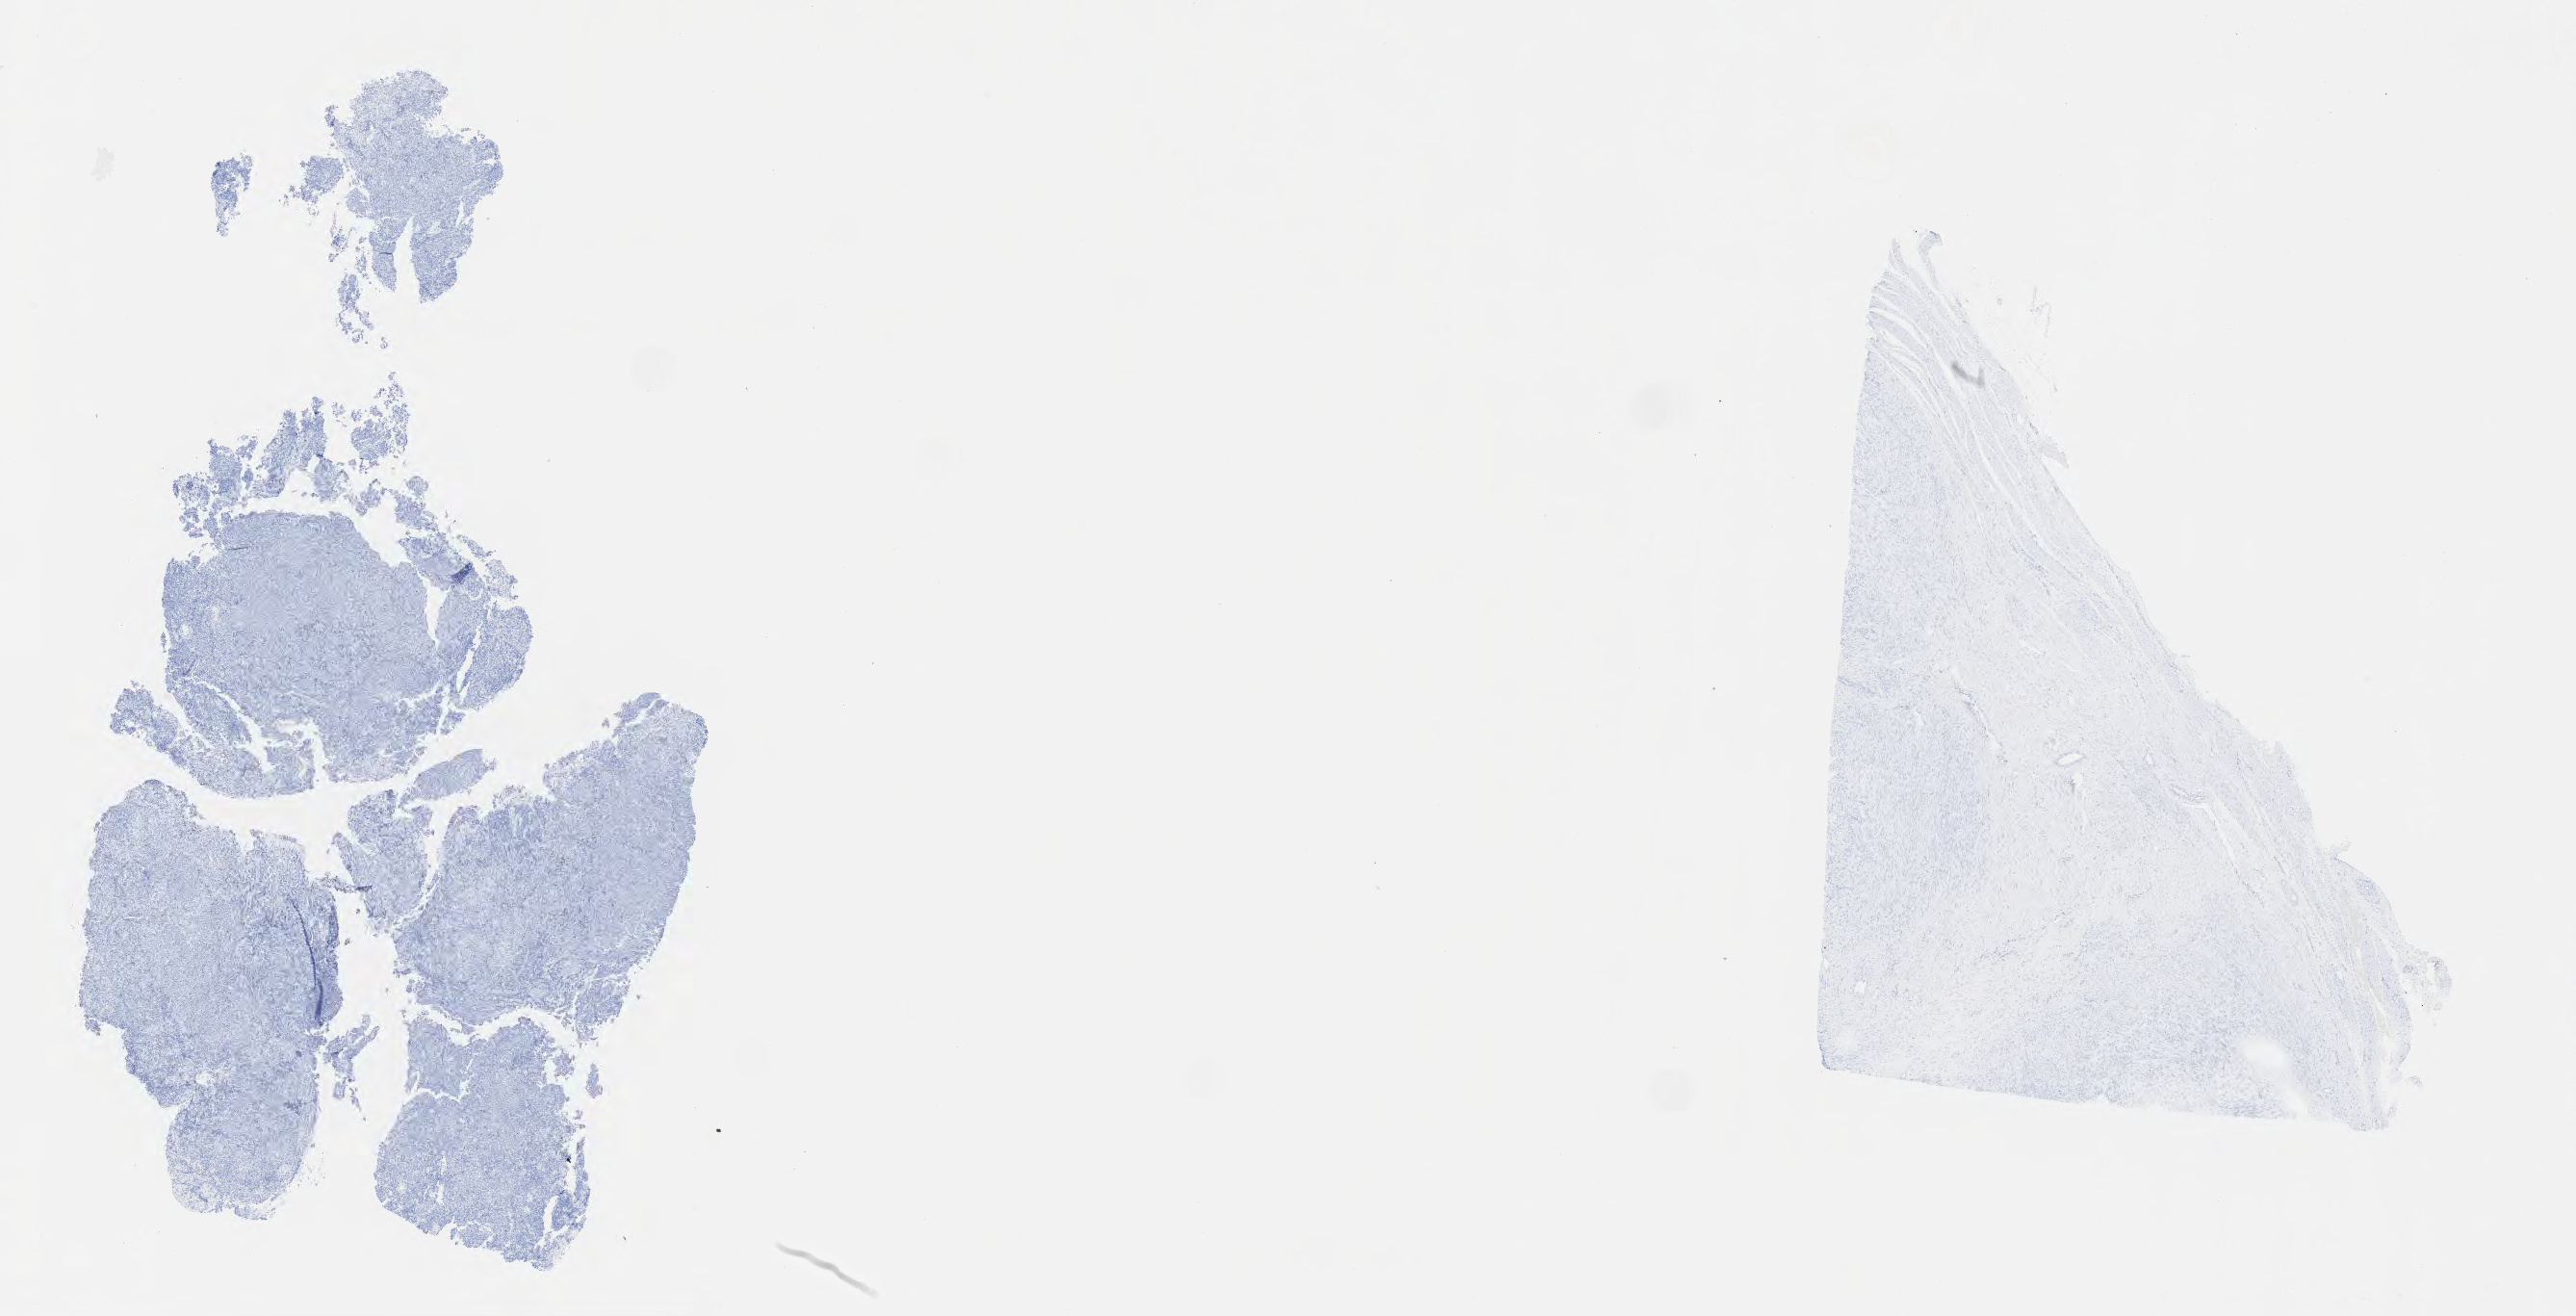
Immunohistochemistry (IHC) whole-slide image stained for progesterone receptor (PR) — whole scanned area (about 21.6 x 11.1 mm) shown as a low-resolution overview. Specimen: tumor tissue. Site: cervix. Patient female; 75 years old.
- diagnosis: Adenocarcinoma, NOS